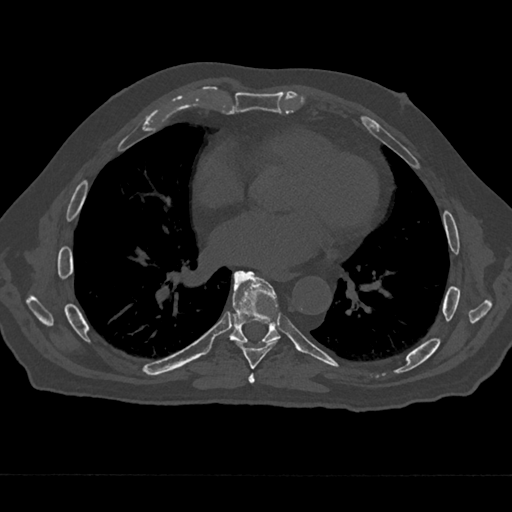
CT including the spine, one axial slice; slice 345 of 797 in the series (ordered by position); 120 kVp; bone window (W 1800 / L 400 HU); 512 × 512 image matrix, field of view 377 × 377 mm. Male patient, age 75 years. From the clinical record (not read from this slice): primary cancer: renal; vertebrae with lytic lesions (as recorded): T4.
Annotated regions visible in this slice (semi-automatically segmented with operator editing):
- T6 vertebra: bounding box [x1, y1, x2, y2] px = [248, 373, 255, 384]
- T7 vertebra: [235, 270, 279, 369]
- T8 vertebra: [230, 271, 280, 343]